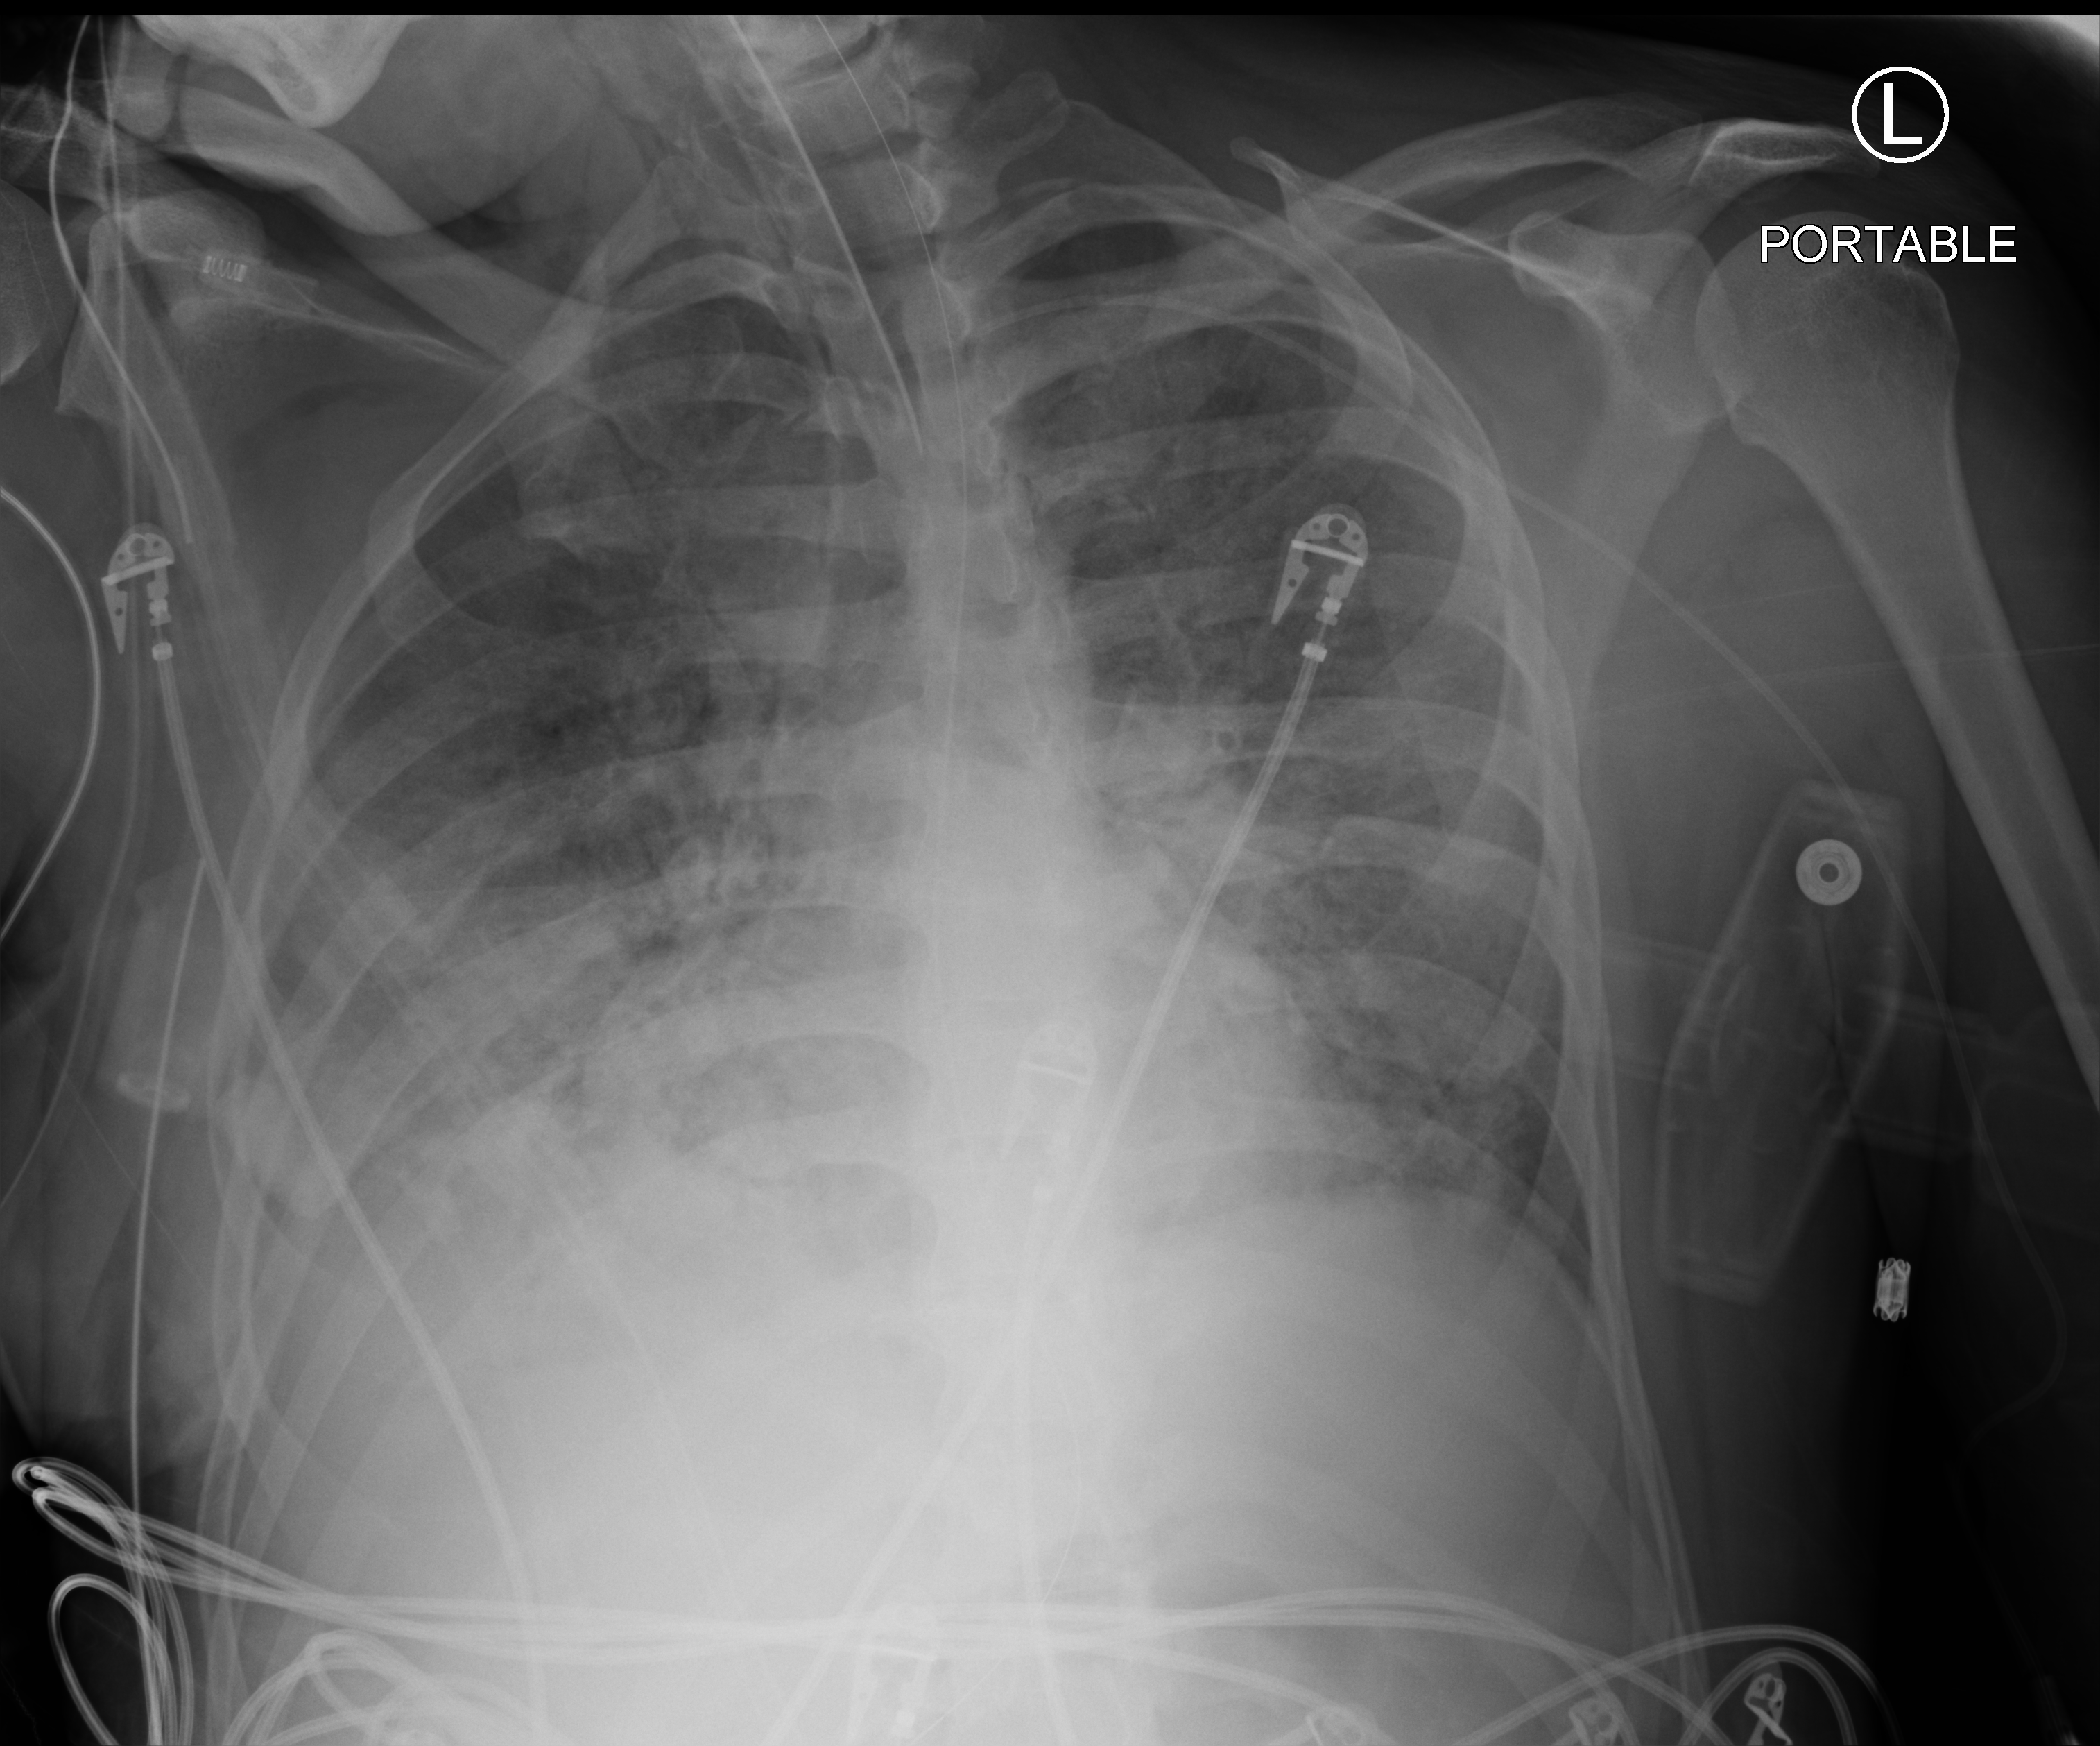
Chest X-ray (portable), anteroposterior (AP) projection. Patient hospitalised with COVID-19; male, aged 18–59 years.
Admission-level facts for this patient (not findings on this image; timing relative to this image not recorded):
- admitted to intensive care during this hospital stay: yes
- chronic kidney disease (admission record): no